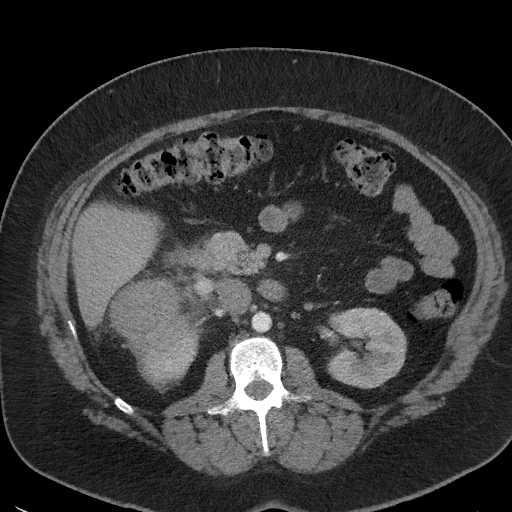
Contrast-enhanced abdominal CT, one axial slice. Position 21 of 56 along the scan axis. Reconstruction kernel I41f/3. 120 kVp. Intravenous contrast given. Soft-tissue window (W 400 / L 40 HU). 5 mm slice thickness. 512 × 512 image matrix, field of view 373 × 373 mm. Patient: female, 35 years. From the clinical record (not read from this slice): diagnosis: adrenocortical carcinoma; tumour side: right adrenal; tumour size at pathology: 15 cm; Ki-67 index: 40 %; stage (as recorded): 2.
Annotated regions visible in this slice (semi-automatically segmented with operator editing):
- mass: bounding box (x1, y1, x2, y2) in pixels: (112, 281, 191, 362)